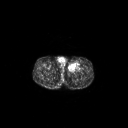
FDG PET of an extremity soft-tissue mass (from a PET/CT study), one axial slice. Slice 264 of 267 in the series (ordered by position). 128 × 128 image matrix, field of view 700 × 700 mm. Male patient, age 63 years. From the clinical record (not read from this slice): histological type: pleiomorphic liposarcoma; grade: high; site of the primary tumour: left thigh.
Structures marked on this image (expert contour drawn on MRI and transferred to this co-registered scan by the dataset authors):
- gross tumour volume including surrounding oedema: bounding box [x1, y1, x2, y2] px = [68, 62, 80, 71]
- gross tumour volume (mass): [68, 63, 77, 69]